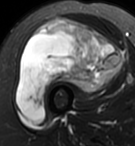
MRI of an extremity soft-tissue mass, one axial slice; slice 52 of 95 in the series (ordered by position); T2-weighted fat-saturated; MR volume resampled by the dataset authors to the PET/CT grid (not the native acquisition matrix); 3.27 mm slice thickness; 135 × 146 image matrix, field of view 132 × 143 mm. Female patient. Case-level facts recorded for this patient, not image findings: histological type: pleiomorphic undifferentiated sarcoma; grade: high; site of the primary tumour: right quadricep.
Structures marked on this image (expert contour drawn on MRI and transferred to this co-registered scan by the dataset authors):
- gross tumour volume including surrounding oedema: bounding box <16,18,125,124> (left, top, right, bottom; pixels)
- gross tumour volume (mass): <16,18,125,124>